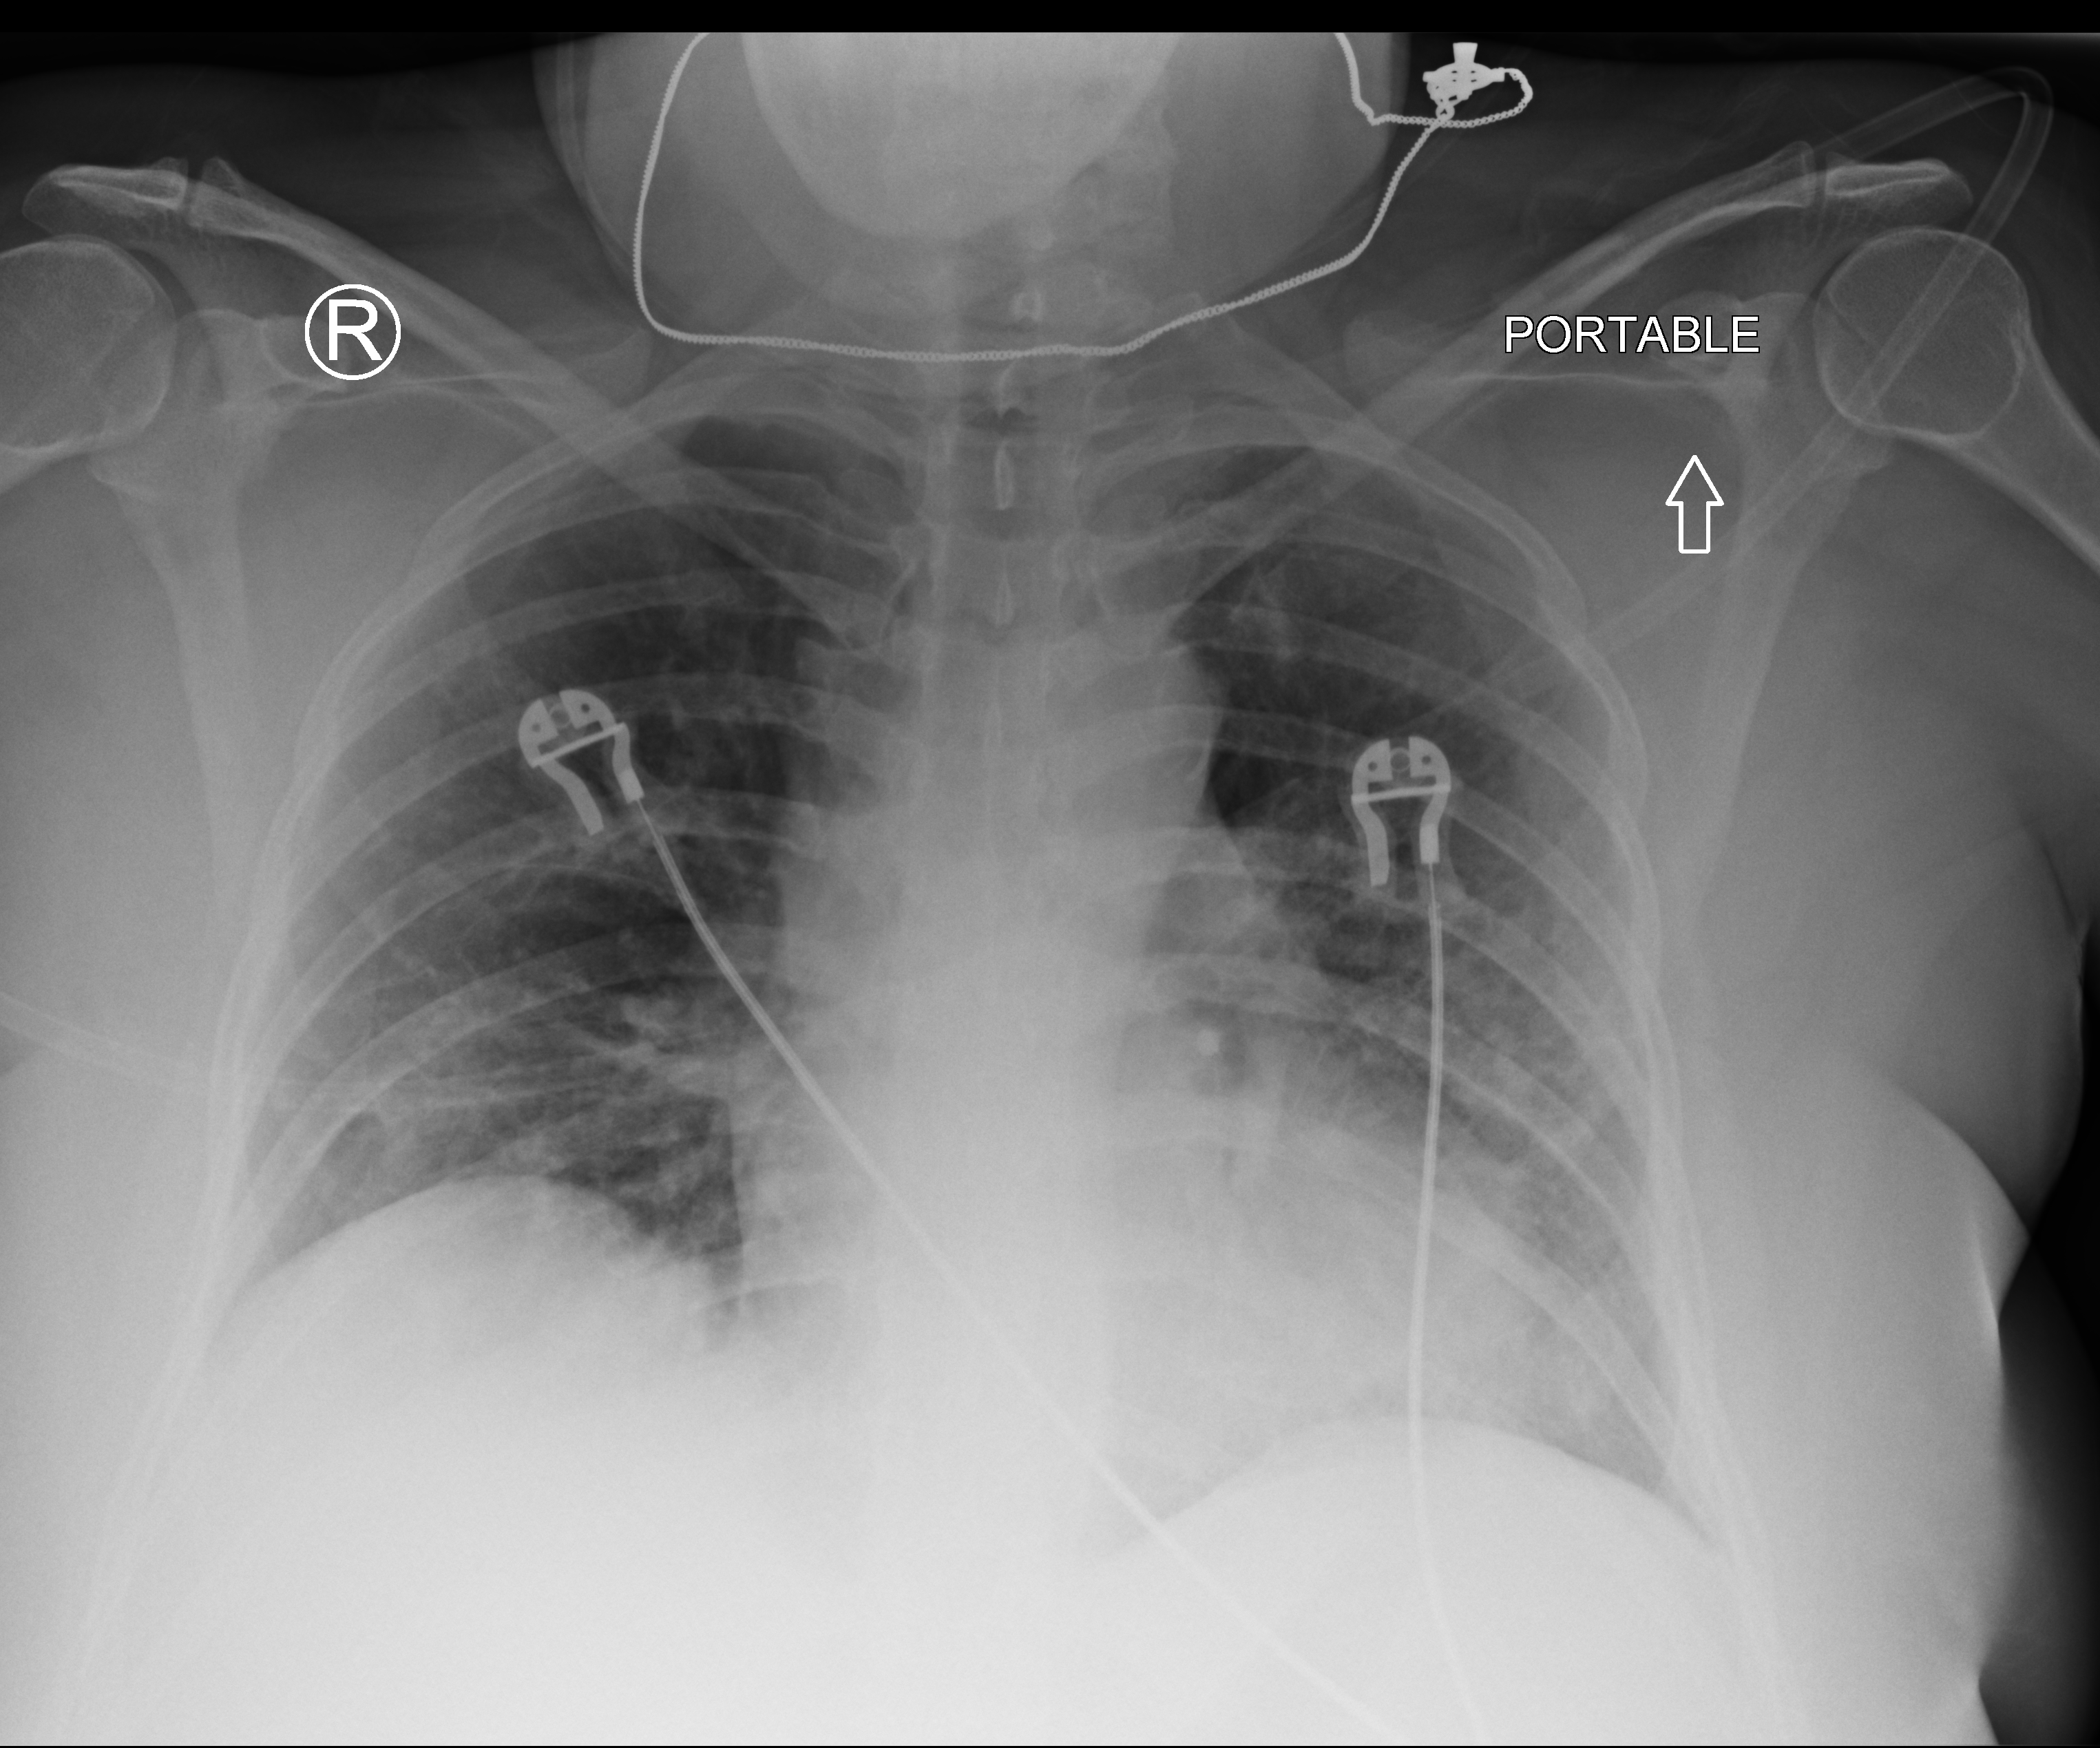
Portable chest radiograph, anteroposterior (AP) projection. Patient hospitalised with COVID-19; female, aged 18–59 years.
Admission-level facts for this patient (not findings on this image; timing relative to this image not recorded):
- hypertension (admission record): no